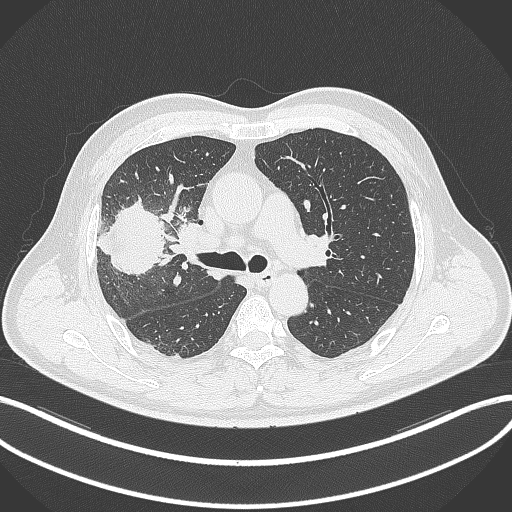
Chest CT, one axial slice; position 210 of 348 along the scan axis; reconstruction kernel B70f; 120 kVp; lung window (W 1500 / L -600 HU); 1 mm slice thickness; 512 × 512 image matrix, field of view 400 × 400 mm. Patient: male, 55 years. From the clinical record (not read from this slice): clinical TNM (as recorded): T3 N2 M1.
Annotated regions visible in this slice (bounding box drawn by a radiologist):
- lung tumour (recorded histology: adenocarcinoma): bounding box (x1, y1, x2, y2) in pixels: (100, 195, 166, 276)